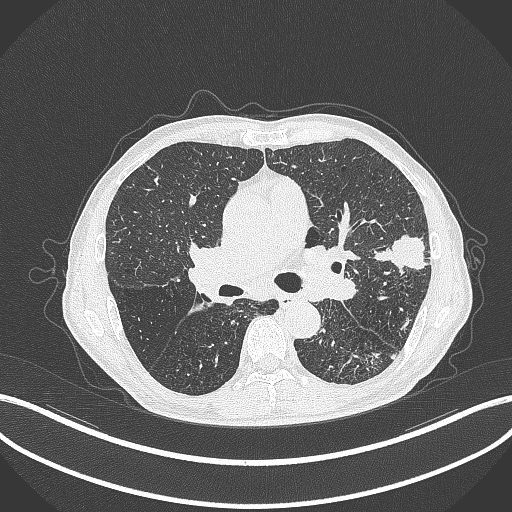
Chest CT, one axial slice; slice 246 of 463 in the series (ordered by position); reconstruction kernel B70f; 120 kVp; lung window (W 1500 / L -600 HU); 512 × 512 image matrix. Male patient, age 74 years. From the clinical record (not read from this slice): clinical TNM (as recorded): T2a N1 M0.
Annotated regions visible in this slice (rectangle marked by the reading radiologist):
- lung tumour (recorded histology: adenocarcinoma): bounding box (x1, y1, x2, y2) in pixels: (374, 228, 433, 274)